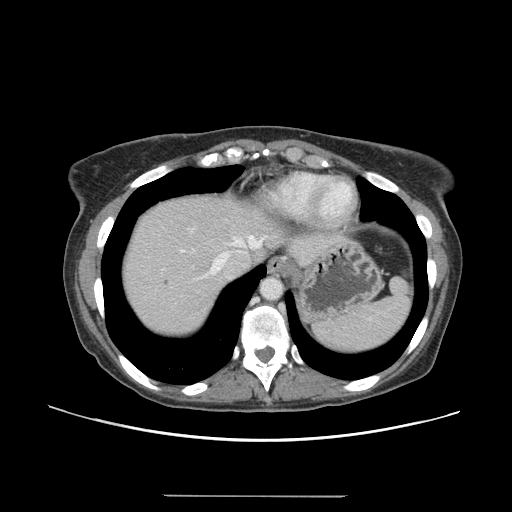
Contrast-enhanced abdominal CT, one axial slice. Position 125 of 144 along the scan axis. 120 kVp. Soft-tissue window (W 400 / L 40 HU). 512 × 512 image matrix. Female patient, age 53 years. From the clinical record (not read from this slice): diagnosis: colorectal cancer liver metastases, imaged before liver resection; multiple liver metastases: yes; largest metastasis: 1.1 cm; disease in both lobes: no.
Structures marked on this image (expert manual segmentation):
- hepatic veins: bounding box [x1, y1, x2, y2] px = [211, 236, 263, 274]
- liver: [122, 195, 279, 337]
- planned liver remnant (the part of the liver to remain after resection): [121, 194, 267, 295]